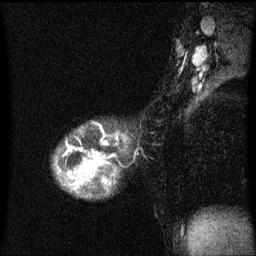
Breast MRI (dynamic contrast-enhanced), one sagittal slice; position 40 of 60 along the scan axis; dynamic contrast-enhanced series, image 2 of 3 at this slice position (ordered by acquisition); 1.5 T; TE 4.2 ms, TR 8 ms; 256 × 256 image matrix, field of view 200 × 200 mm. Female patient, age 36 years.
Annotated regions visible in this slice (semi-automatic segmentation, software-assisted and operator-edited):
- analysis volume of interest (the breast-tissue region the enhancement analysis was run in; not a lesion): bounding box (x1, y1, x2, y2) in pixels: (56, 140, 110, 169)
- tumour enhancement mask (voxels above the 70 % enhancement threshold inside the analysis volume of interest): (65, 142, 110, 169)